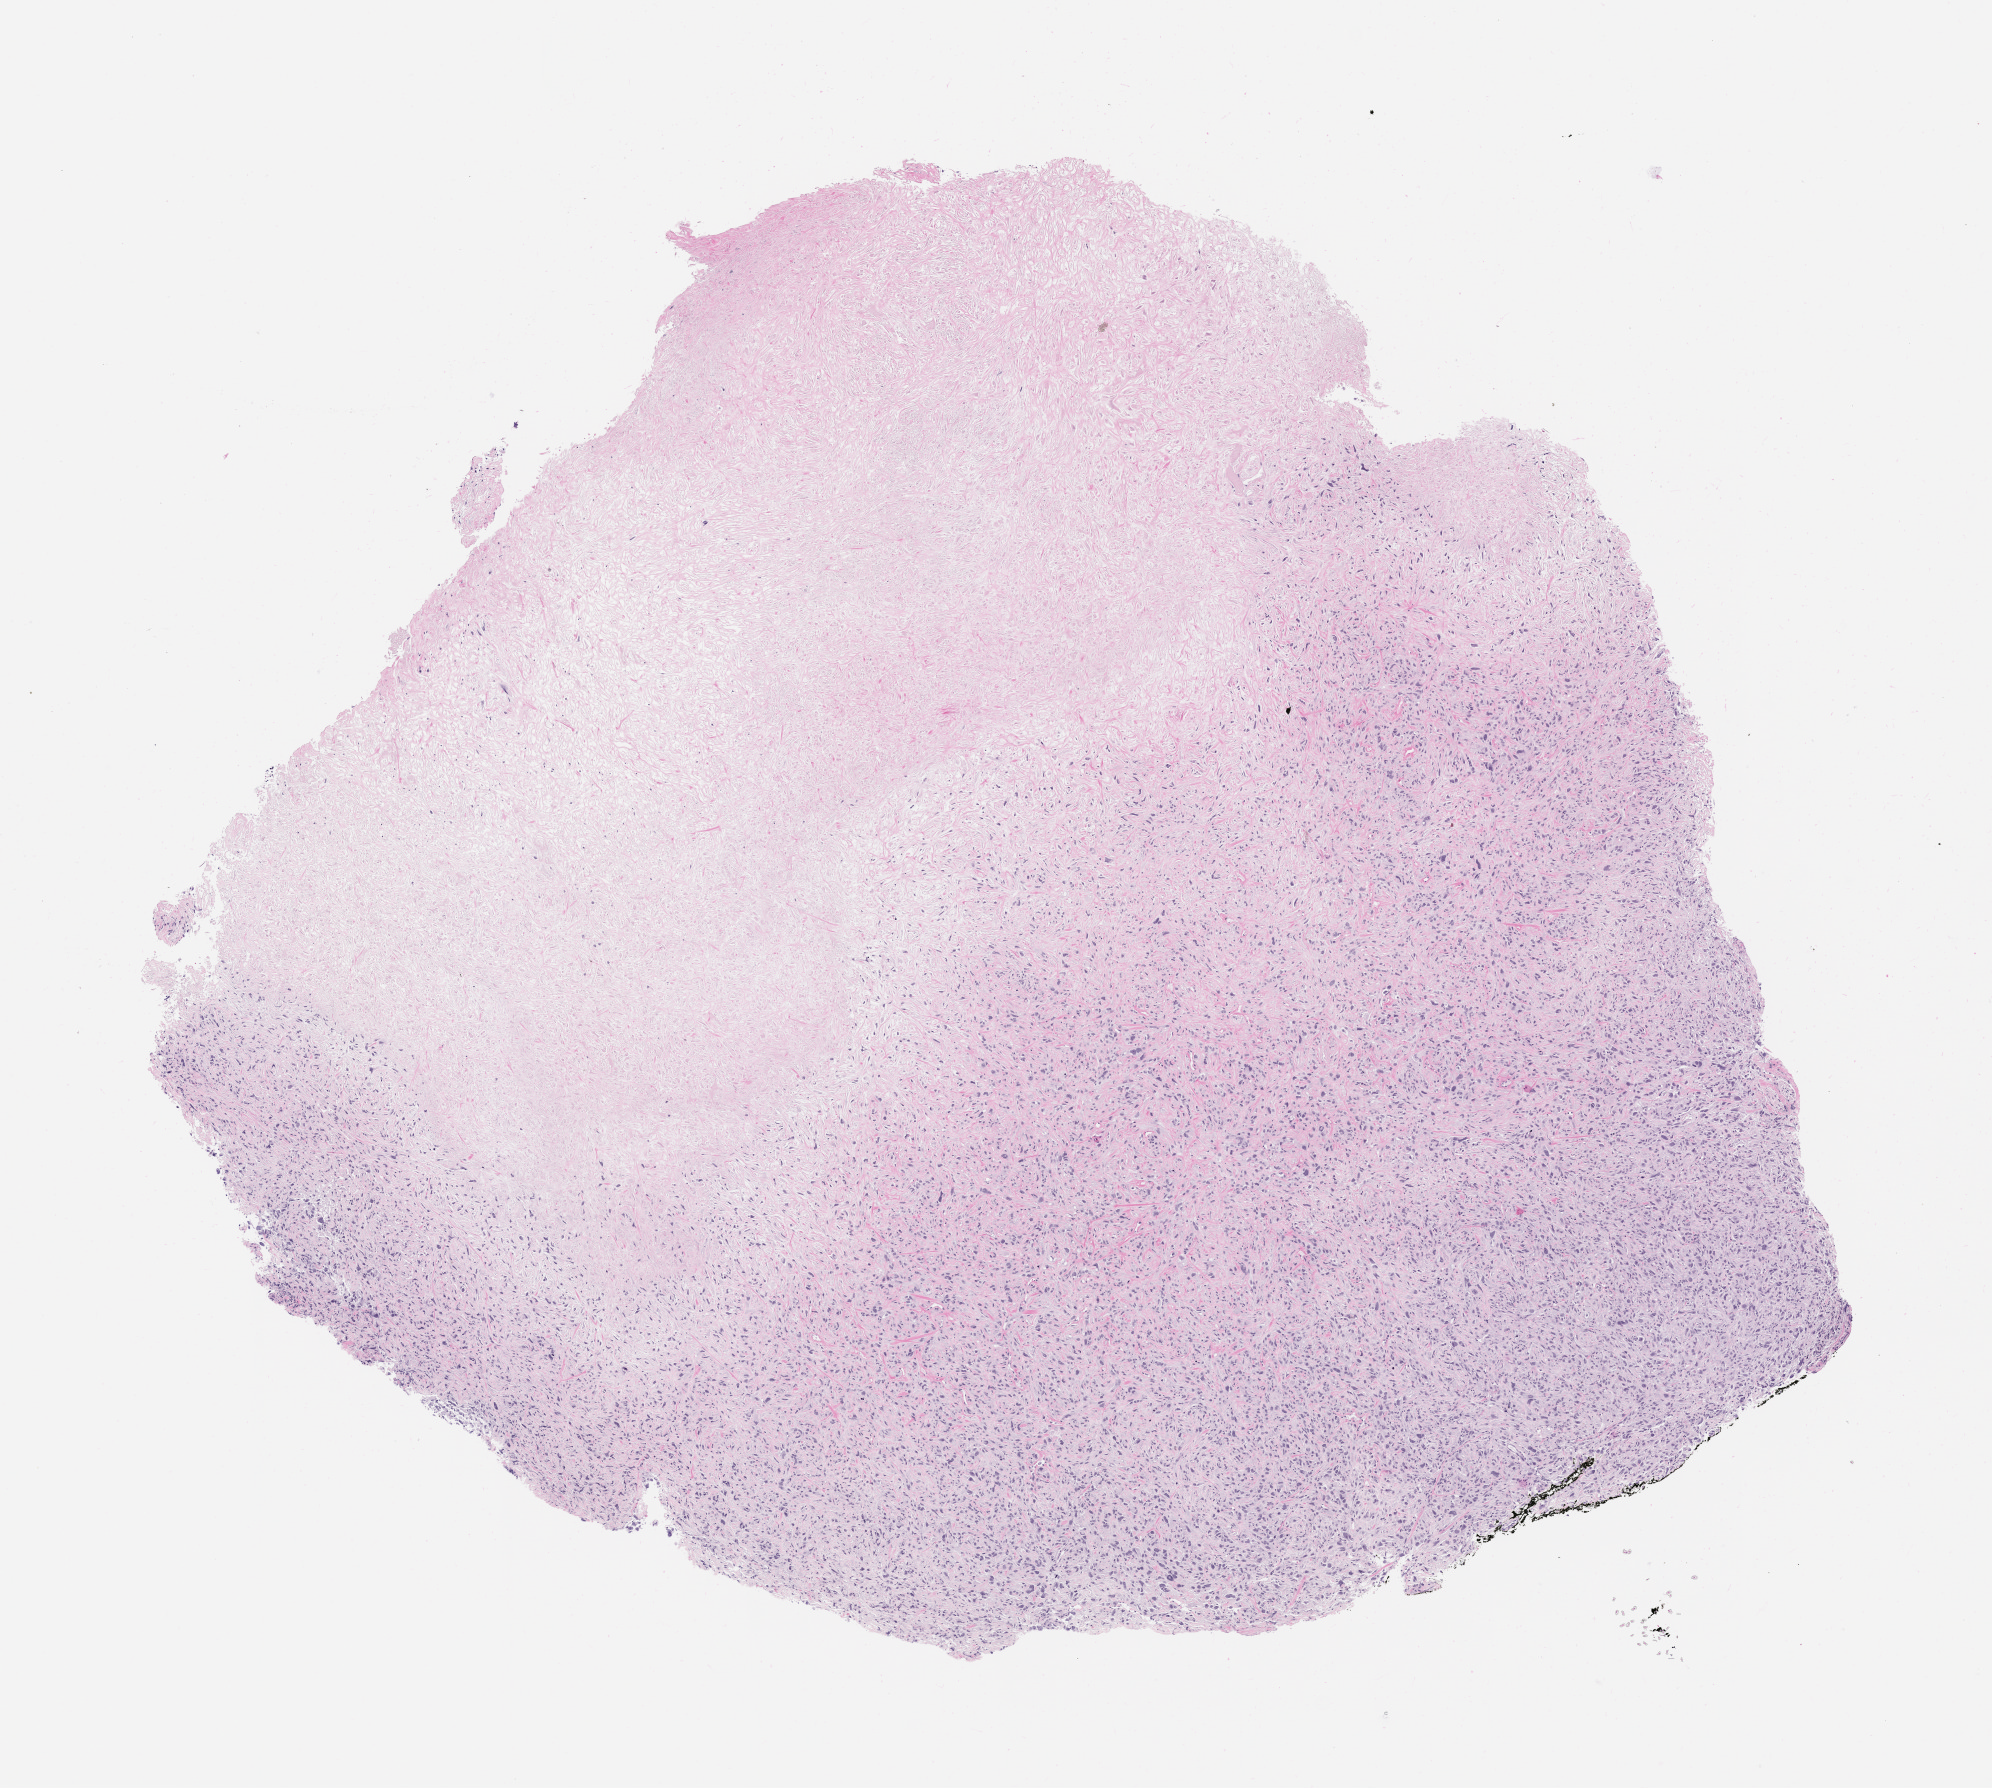
Haematoxylin and eosin whole-slide image of a patient-derived xenograft (PDX) tumor grown in a mouse, a low-resolution overview of the entire scanned area, about 8.0 x 7.2 mm. Formalin-fixed, paraffin-embedded (FFPE) tissue. Tumor site category: musculoskeletal.
Originating patient diagnosis: Spindle Cell Sarcoma.